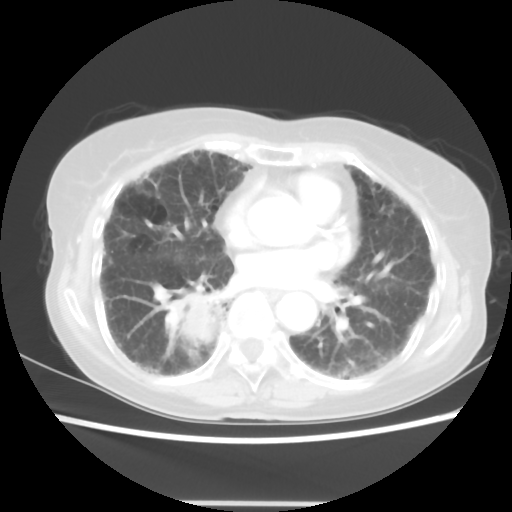
Chest CT, one axial slice; position 25 of 52 along the scan axis; reconstruction kernel STANDARD; 120 kVp; lung window (W 1500 / L -600 HU); 5 mm slice thickness; 512 × 512 image matrix. Female patient, age 71 years. From the clinical record (not read from this slice): clinical TNM (as recorded): T3 N0 M0.
Structures marked on this image (bounding box drawn by a radiologist):
- lung tumour (recorded histology: squamous cell carcinoma): bounding box [x1, y1, x2, y2] px = [166, 289, 223, 356]